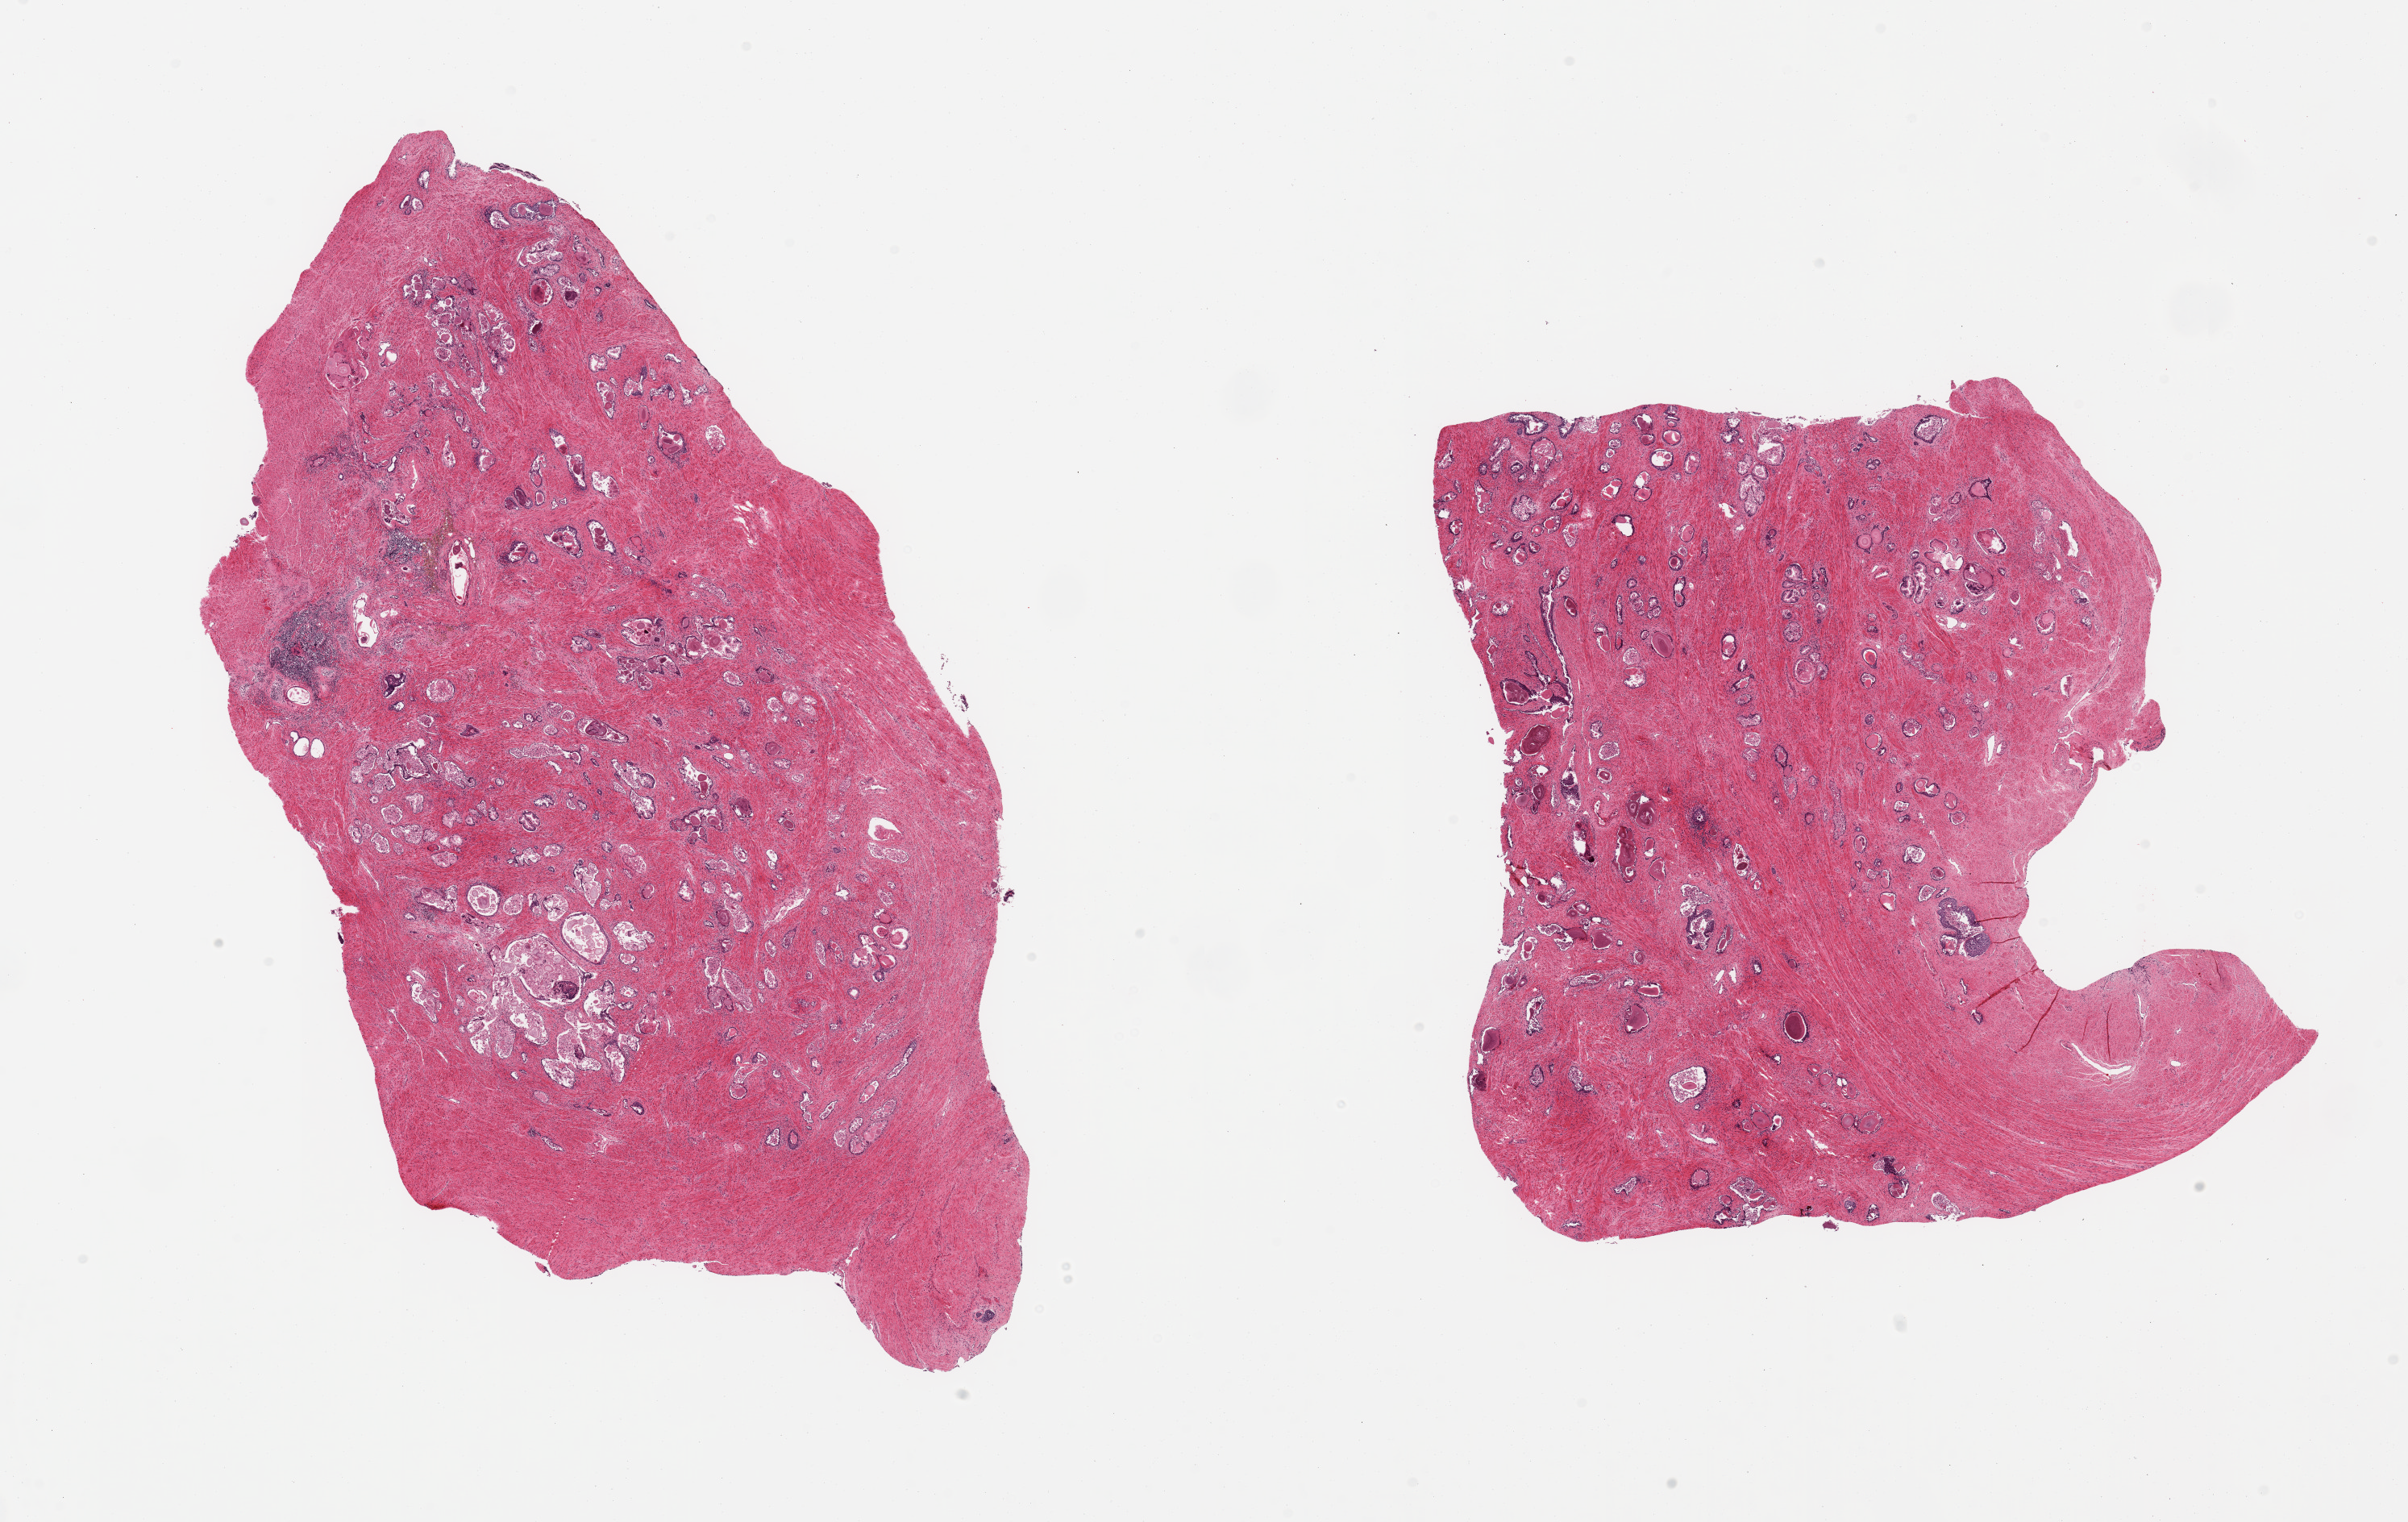
Whole-slide image, H&E stain, brightfield, shown as a low-resolution overview of the whole scanned area (about 23.6 x 14.9 mm); PAXgene-fixed paraffin-embedded (PFPE) section; section of prostate (target tissue); donor tissue sample. Donor sex: male.
- review note (as recorded): 2 pieces; glands autolyzed (3), stroma intact (1)